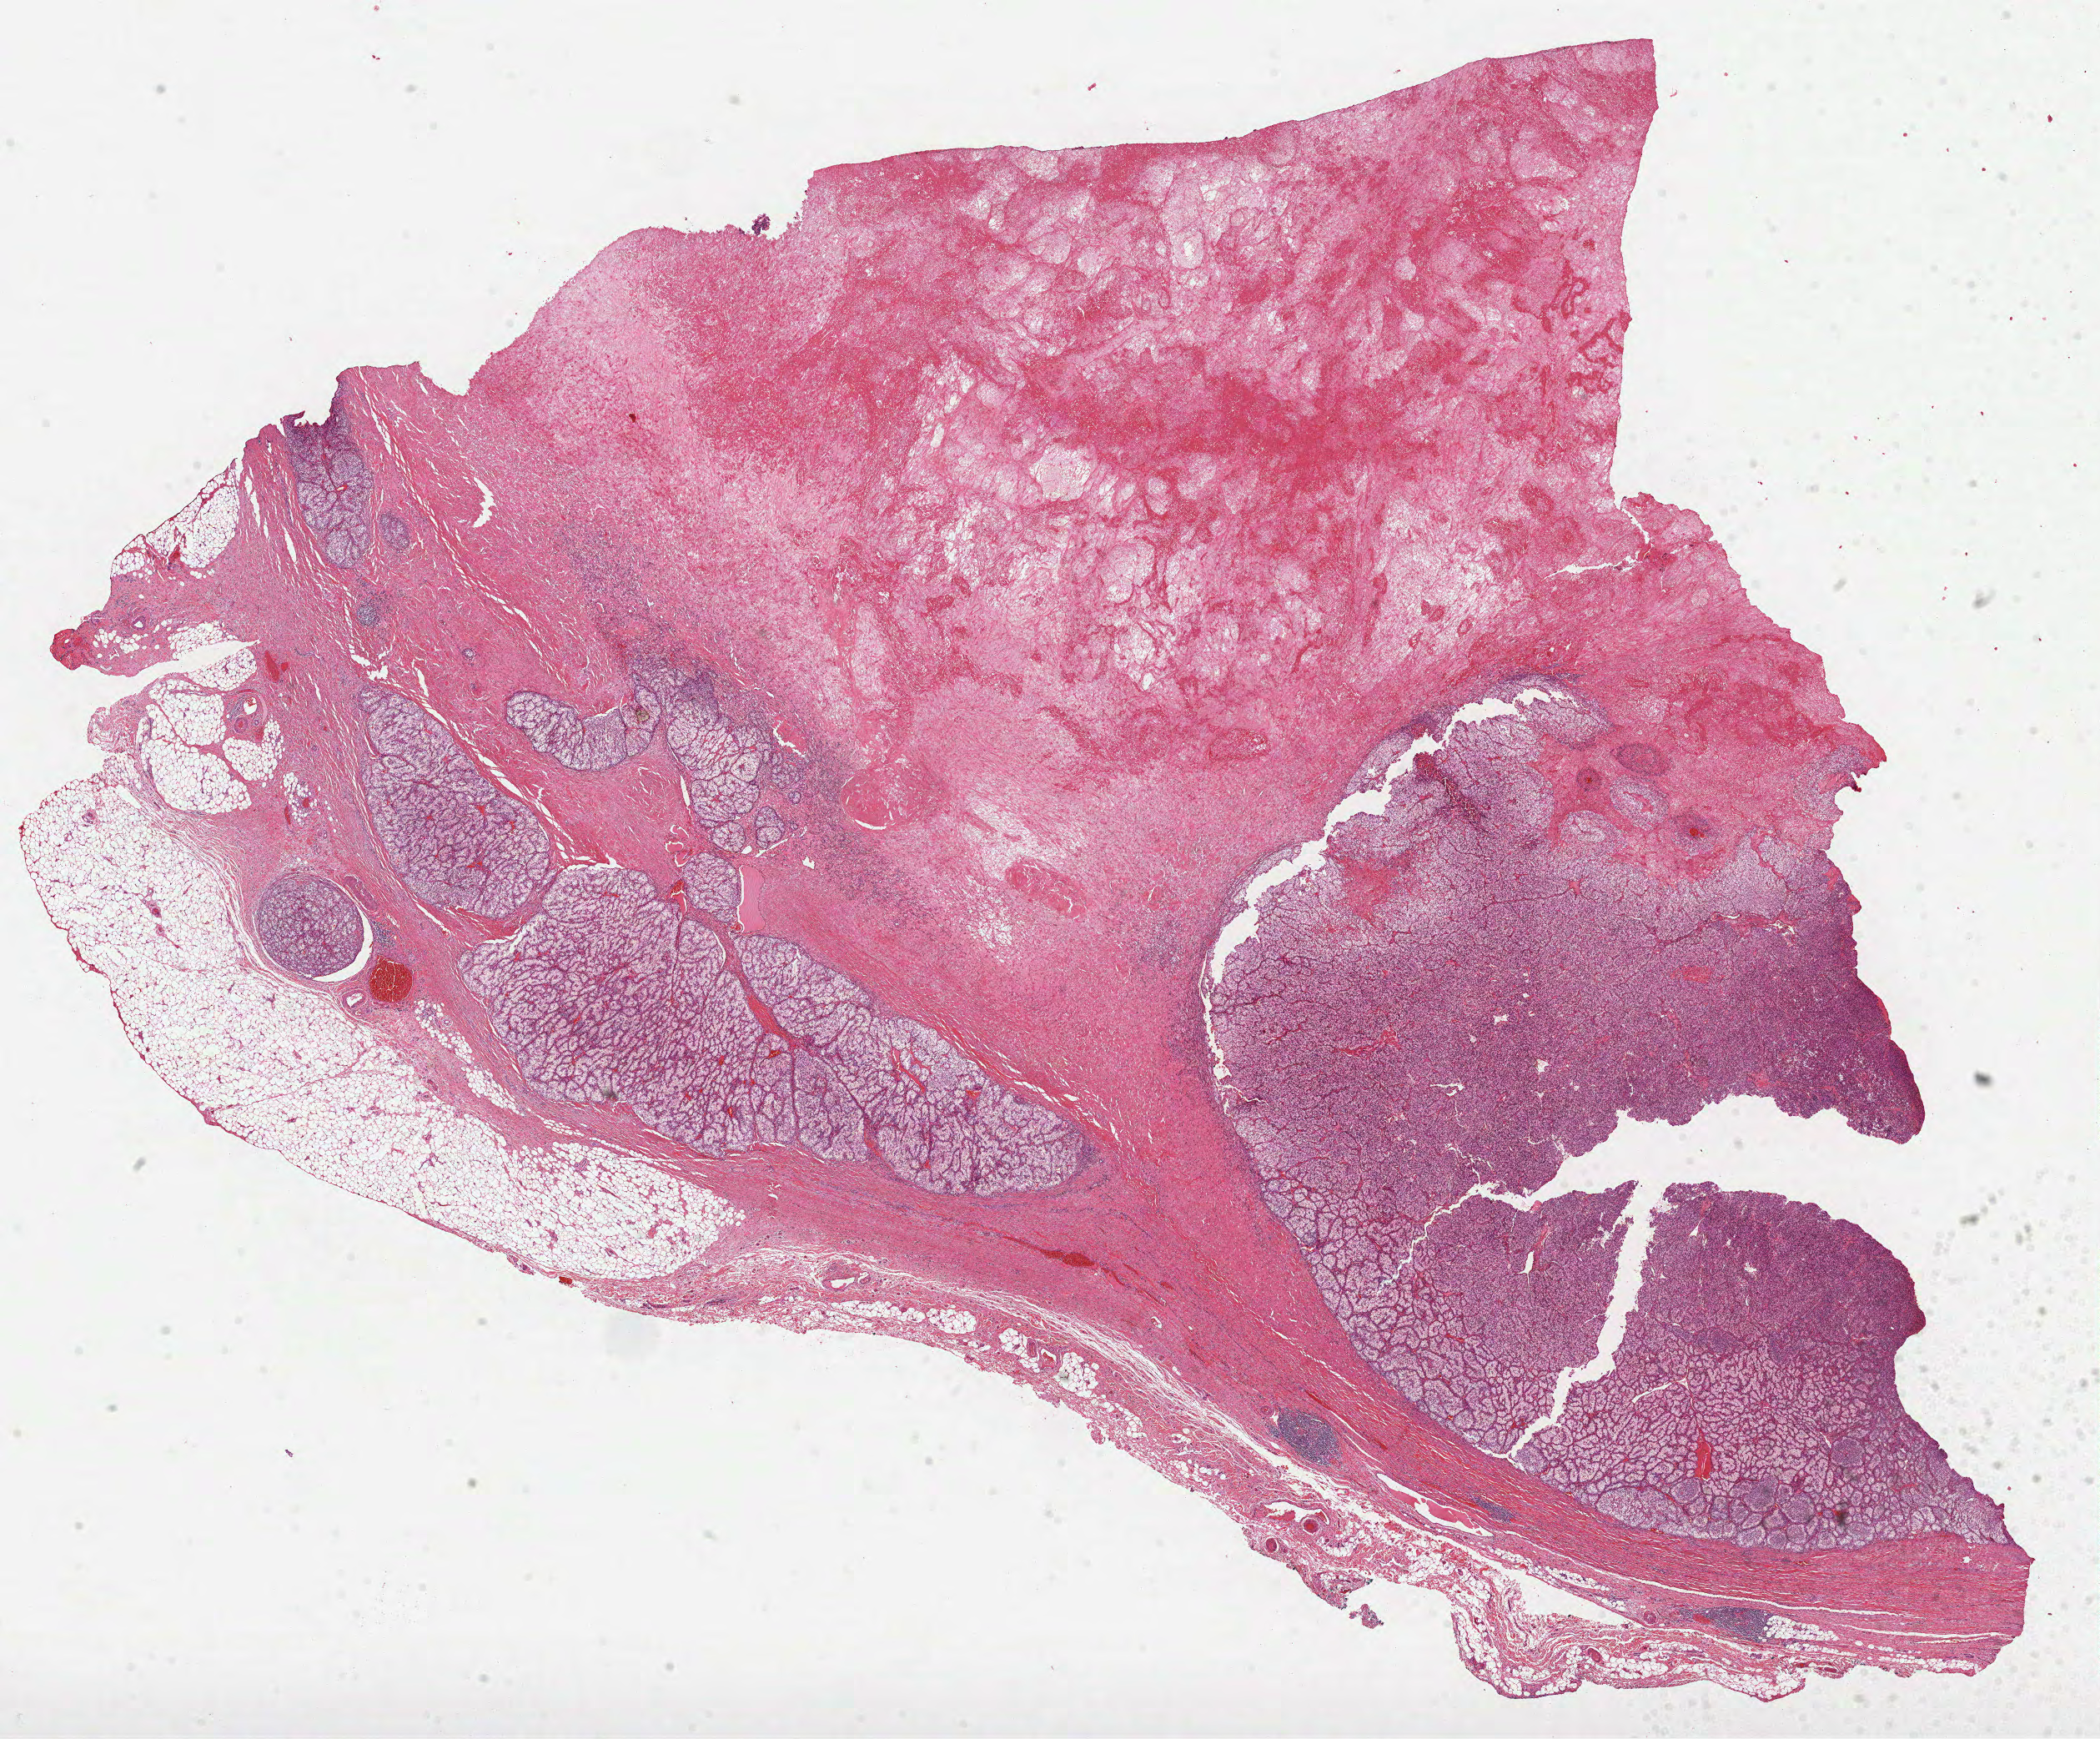
Digitized H&E-stained tissue section (whole slide), whole scanned area (about 20.3 x 16.8 mm, acquisition: 40x scan) shown as a low-resolution overview, FFPE section, primary tumour sample from the kidney. Male patient; age at initial diagnosis 48 years. Histologic grade: G3 (poorly differentiated).
Diagnosis: Clear cell adenocarcinoma, NOS. AJCC pathologic stage: III (5th edition).